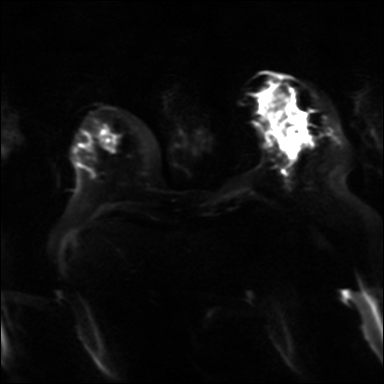
Breast MRI, one axial slice. Slice 10 of 36 in the series (ordered by position). Diffusion-weighted series; image 2 of 4 stored at this slice position (different b-values; order by instance number). 3 T. 4 mm slice thickness. 384 × 384 image matrix. Female patient.
Annotated regions visible in this slice (outlined manually by an expert reader):
- tumour on diffusion-weighted imaging: bounding box [x1, y1, x2, y2] px = [288, 124, 309, 144]